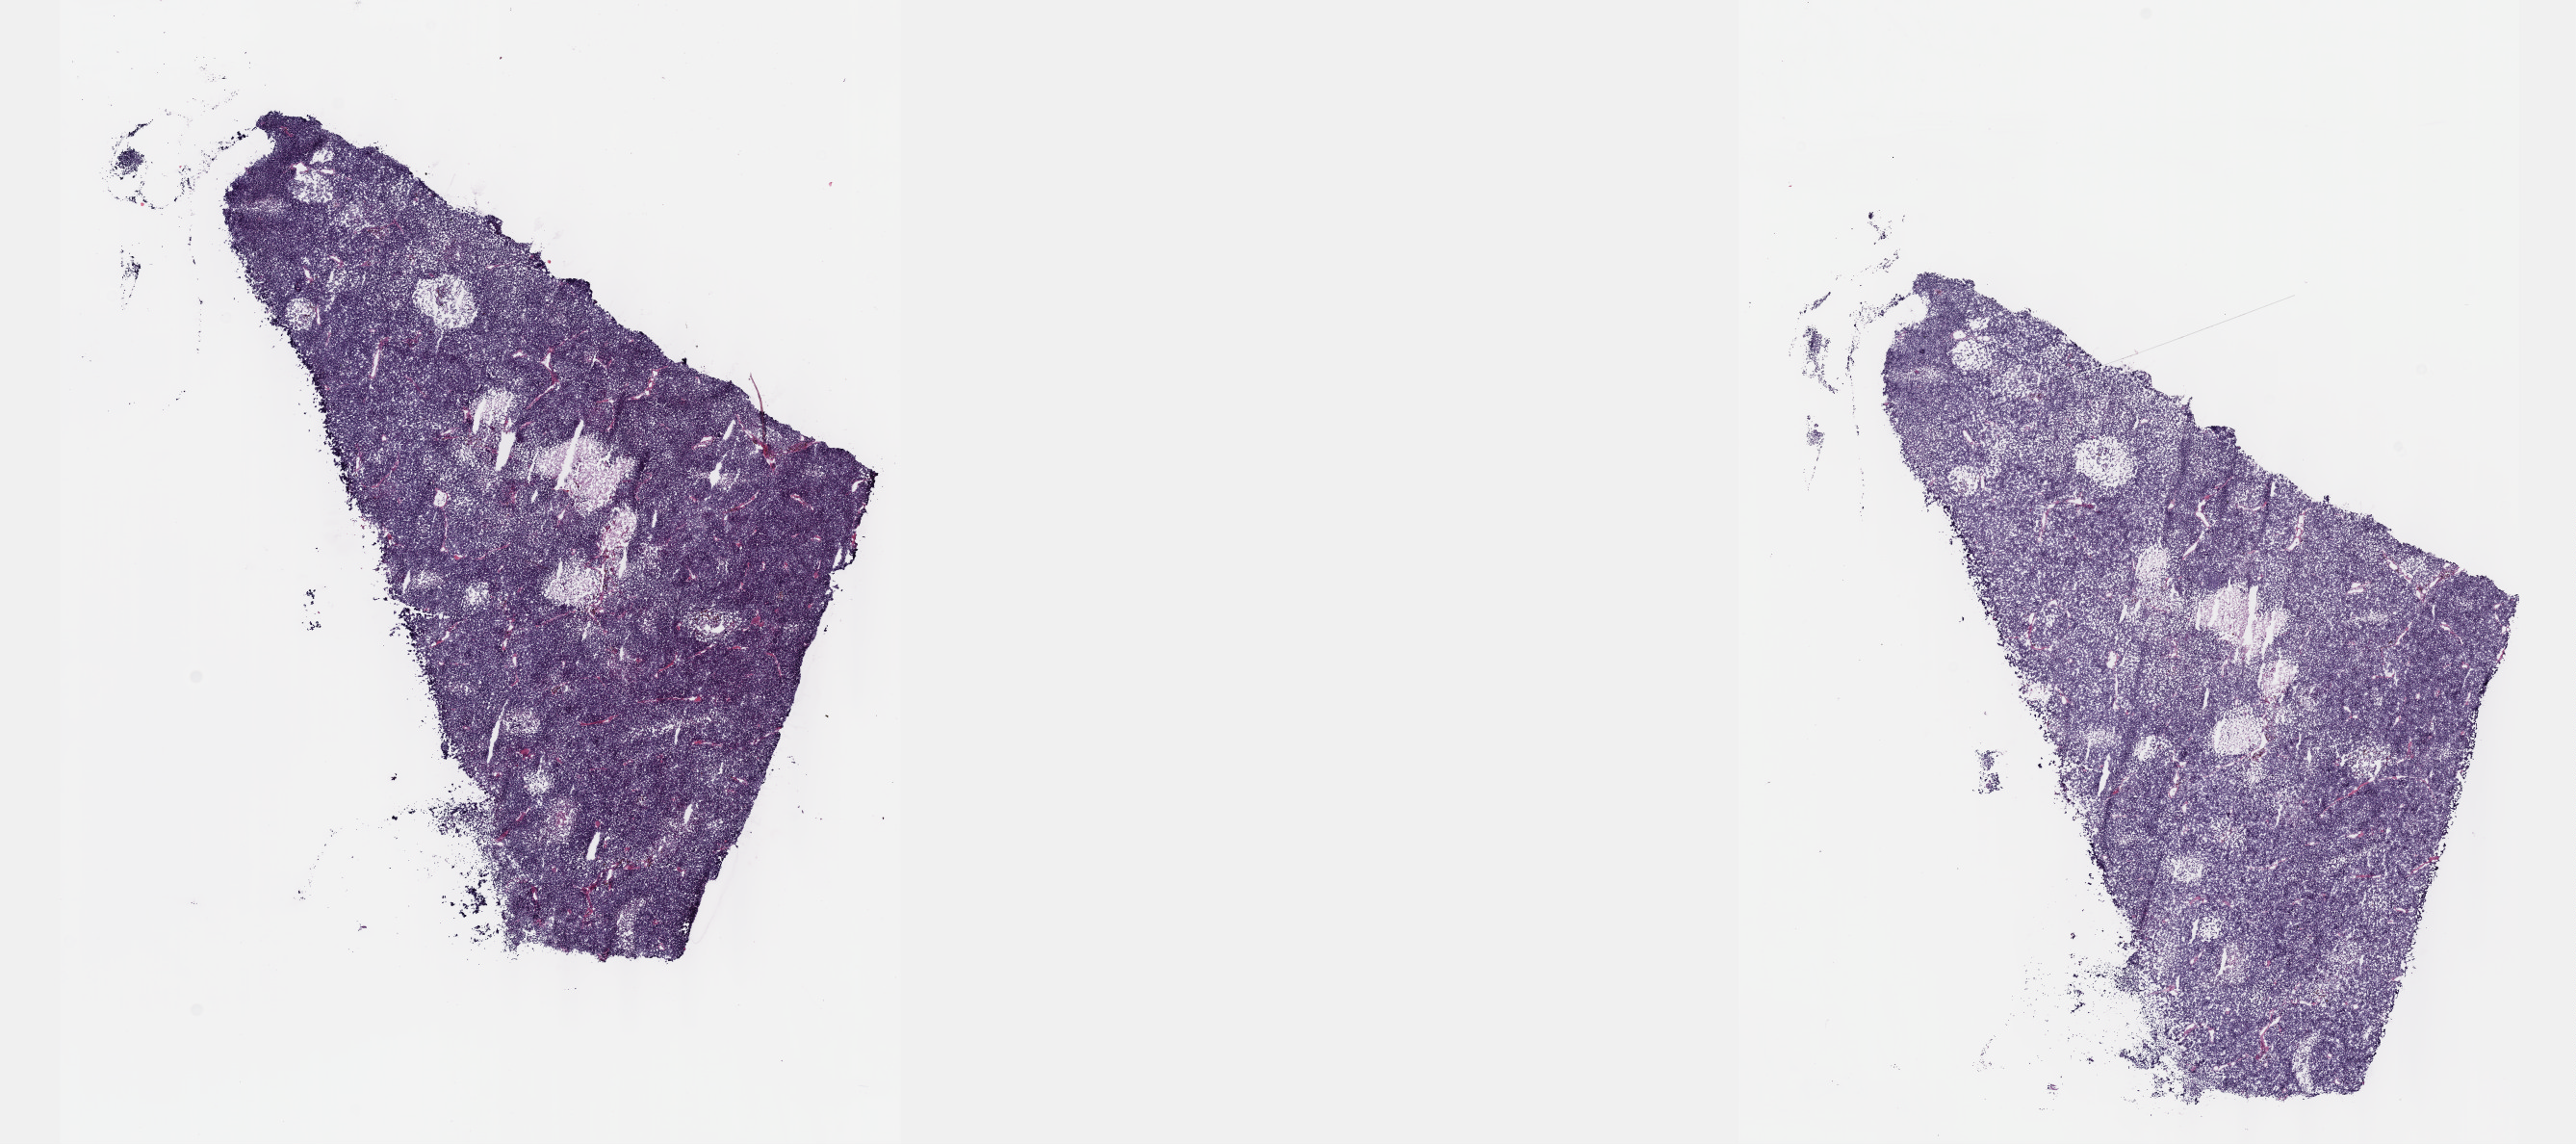
Digitized Hematoxylin and eosin (H&E) stained tissue section (whole slide), shown as a low-resolution overview of the whole scanned area (about 21.6 x 9.6 mm, slide scanned at 40x); frozen section from the top of the tissue portion; thymus, primary tumour sample. Patient: female, age at initial diagnosis 68 years. Pathologist review of this section (percent, as recorded): tumour cells 100%, tumour nuclei 80%, normal cells 0%, stromal cells 0%, necrosis 0%. Inflammatory infiltration, as recorded: lymphocyte infiltration 1%, monocyte infiltration 0%, neutrophil infiltration 0%.
Histologic diagnosis: Thymoma, type B1, NOS.